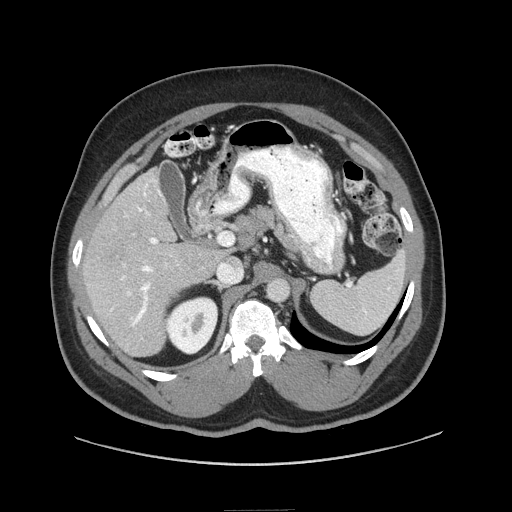
Contrast-enhanced abdominal CT (liver protocol), one axial slice; slice 44 of 87 in the series (ordered by position); 140 kVp; soft-tissue window (W 400 / L 40 HU); 2.5 mm slice thickness; 512 × 512 image matrix, field of view 440 × 440 mm. Case-level facts recorded for this patient, not image findings: diagnosis: hepatocellular carcinoma (patient treated with transarterial chemoembolisation; whether this scan precedes or follows treatment is not stated here); TNM stage (as recorded): Stage-II; Child-Pugh class: A.
Outlined on this slice (semi-automatic segmentation, software-assisted and operator-edited):
- liver parenchyma outside the tumour (the mass and vessels are separate outlines, so this box may not span the whole liver): box from (x=82, y=168) to (x=224, y=356) px
- liver vessels: (x=110, y=179)–(x=168, y=327)